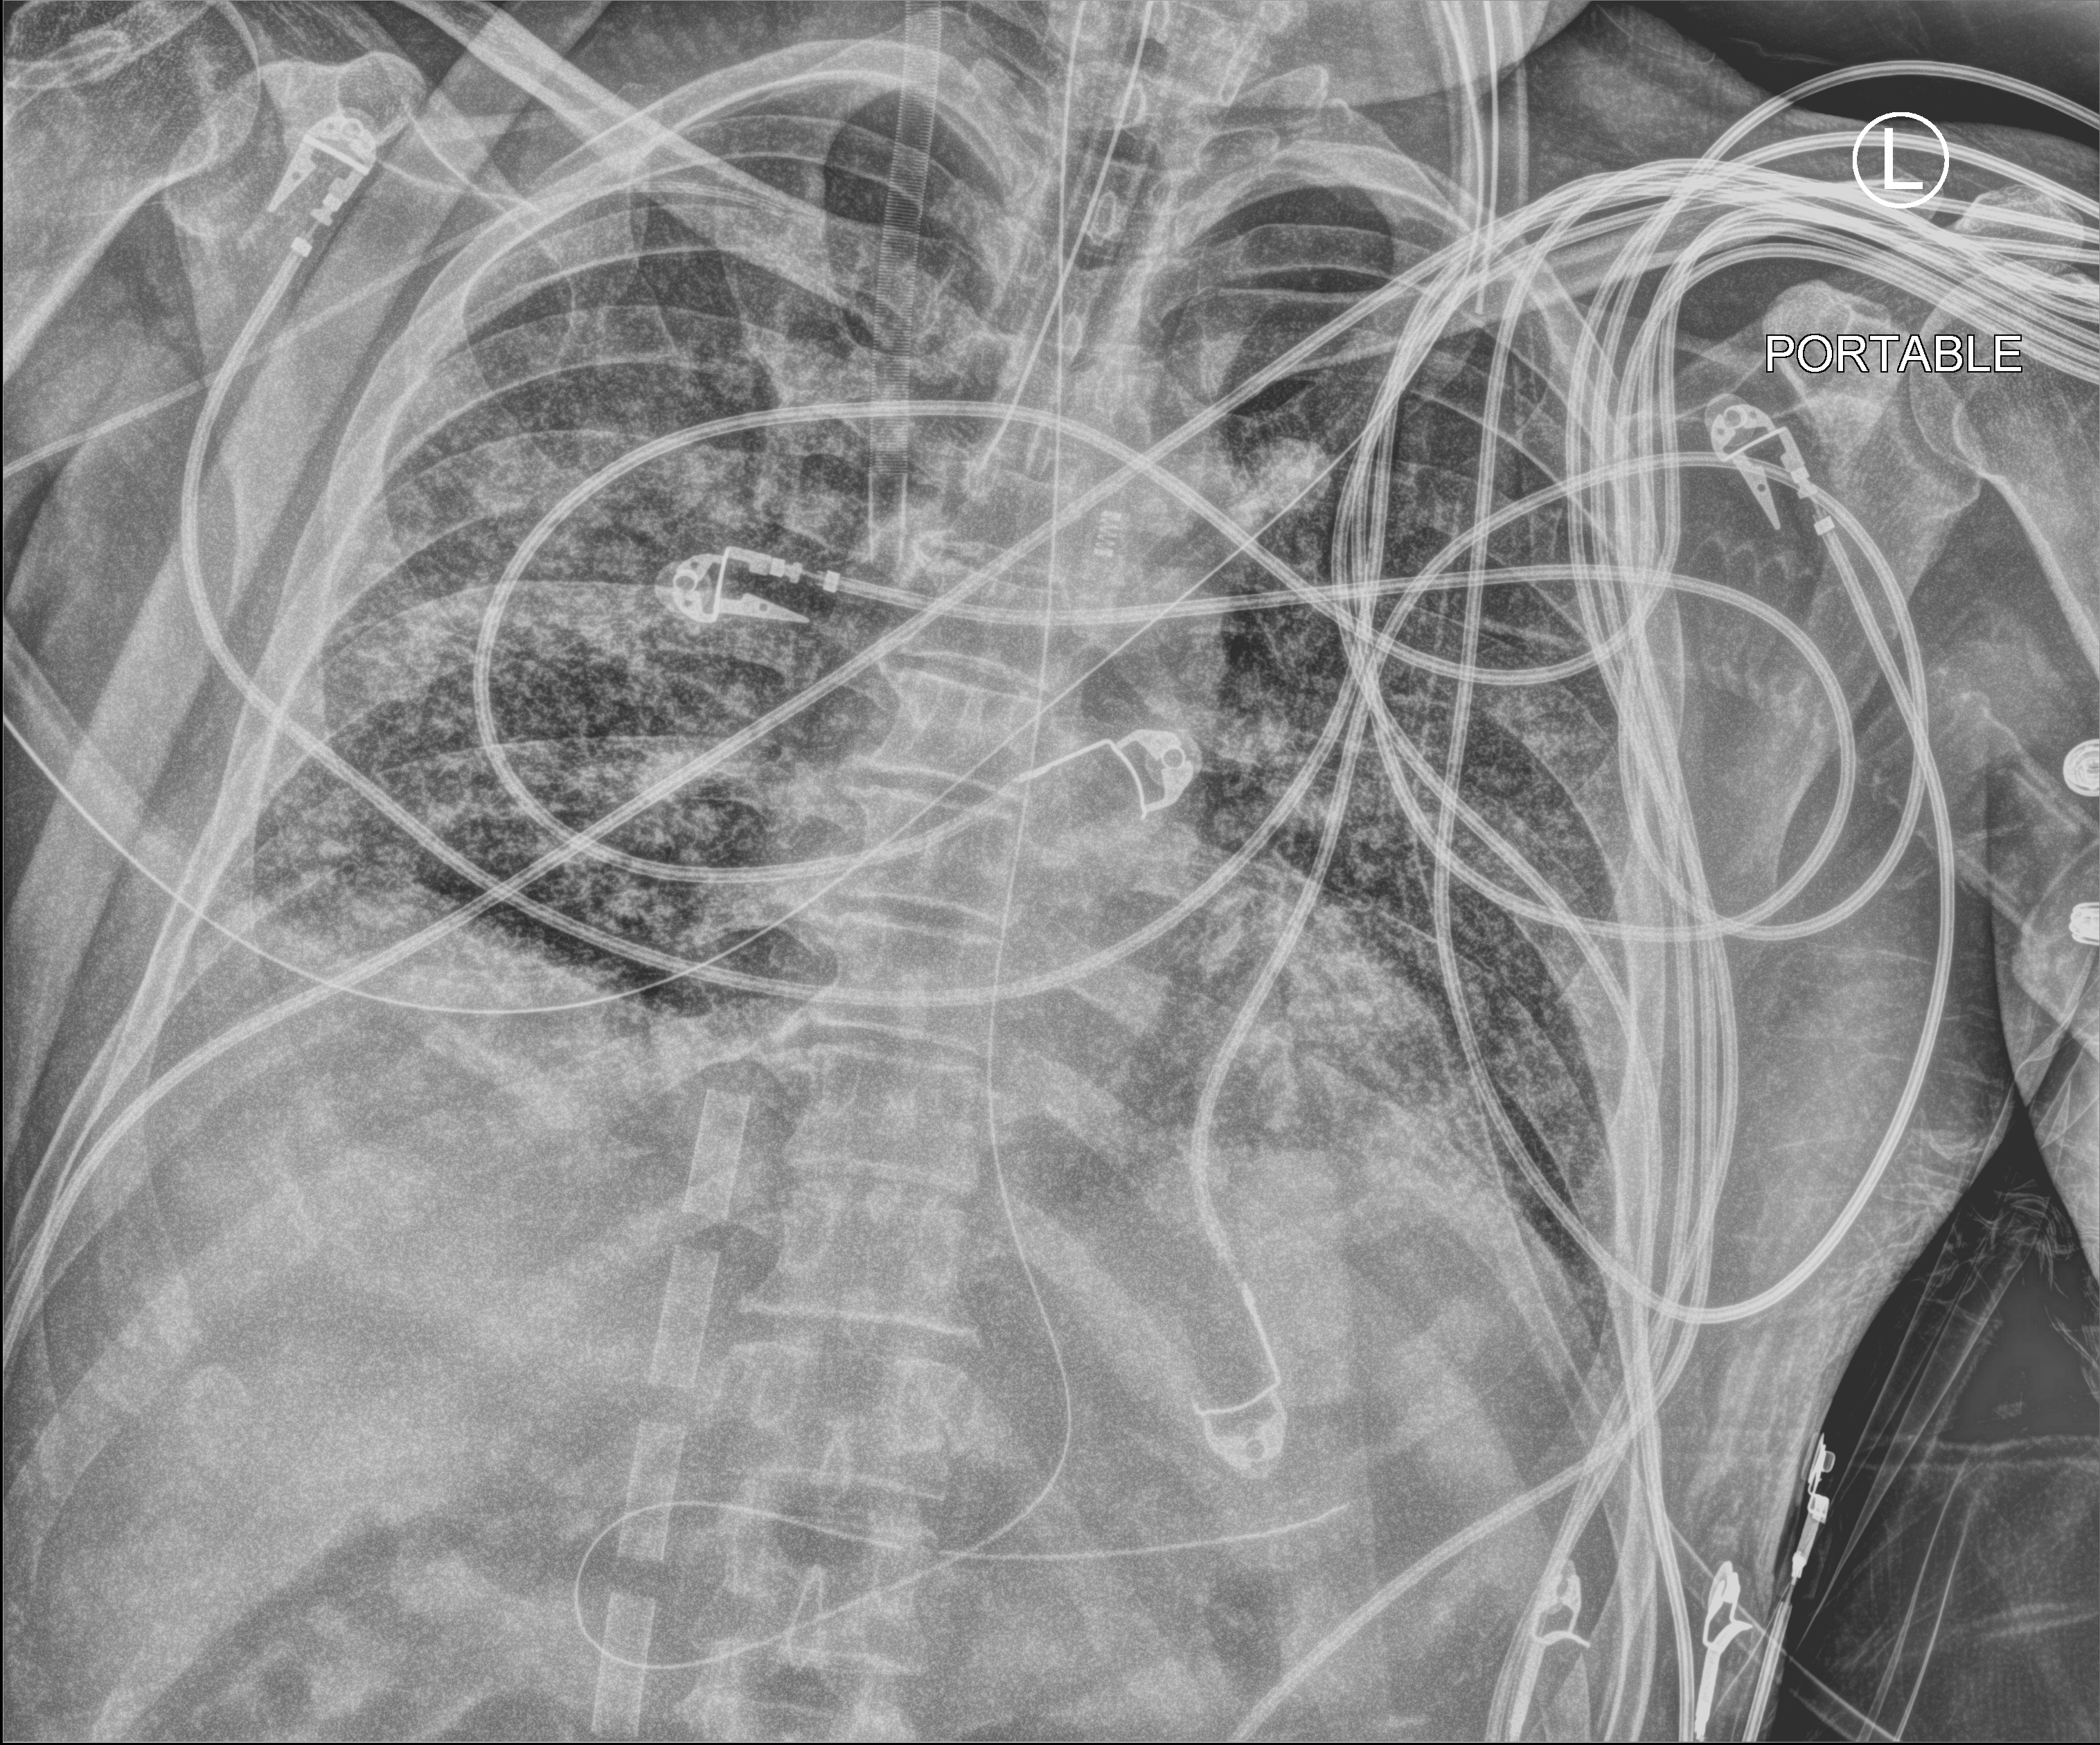
Portable chest radiograph; anteroposterior (AP) projection. Male patient hospitalised with COVID-19, age 18–59 years.
From the hospital-stay record, not from the radiograph (when in the stay this image was taken is not recorded):
- mechanically ventilated during this hospital stay: yes